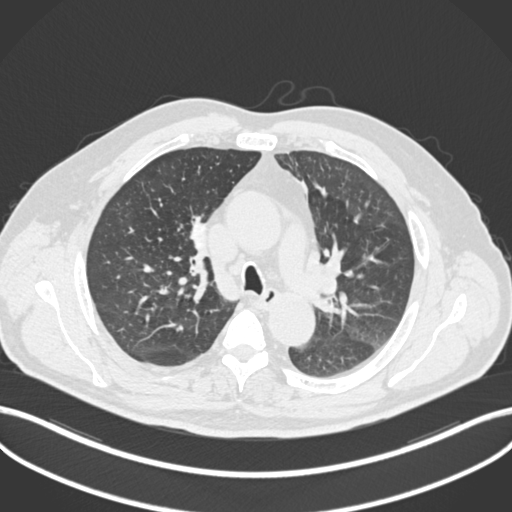
Chest CT, one axial slice; position 129 of 255 along the scan axis; lung window (W 1500 / L -600 HU); 1 mm slice thickness; 512 × 512 image matrix, field of view 400 × 400 mm. Male patient, age 60 years. Case-level facts recorded for this patient, not image findings: clinical TNM (as recorded): T1b N1 M0.
Annotated regions visible in this slice (bounding box drawn by a radiologist):
- lung tumour (recorded histology: squamous cell carcinoma): bounding box (x1, y1, x2, y2) in pixels: (183, 206, 221, 288)